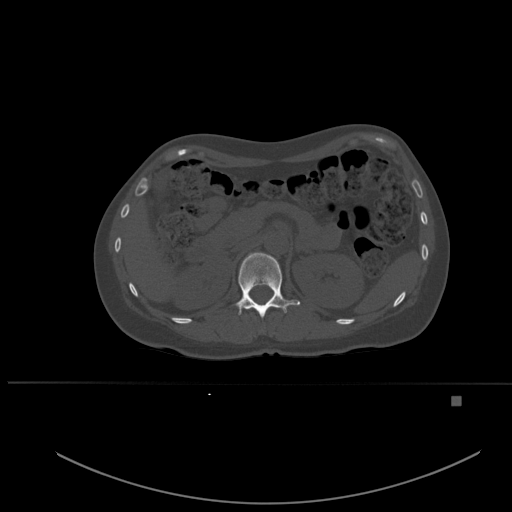
CT including the spine, one axial slice. Slice 253 of 651 in the series (ordered by position). Bone window (W 1800 / L 400 HU). 512 × 512 image matrix, field of view 443 × 443 mm. Patient: female, 49 years. Case-level facts recorded for this patient, not image findings: primary cancer: breast; vertebrae with lytic lesions (as recorded): L3, T12, L4.
Outlined on this slice (semi-automatic segmentation, software-assisted and operator-edited):
- T12 vertebra: bounding box [x1, y1, x2, y2] px = [235, 252, 300, 318]